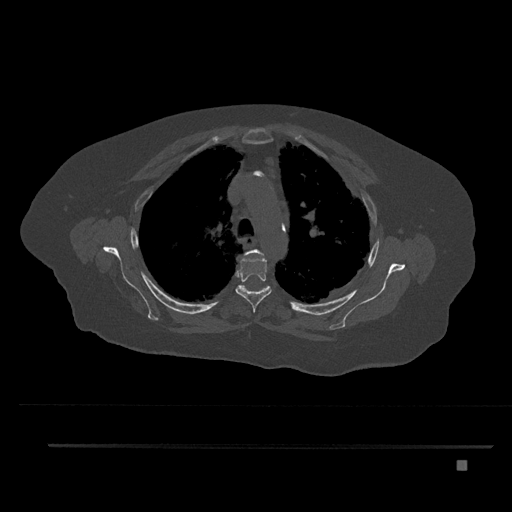
CT including the spine, one axial slice; slice 601 of 797 in the series (ordered by position); reconstruction kernel Br40s/3; bone window (W 1800 / L 400 HU); 0.5 mm slice thickness; 512 × 512 image matrix, field of view 437 × 437 mm. Female patient, age 76 years. Case-level facts recorded for this patient, not image findings: primary cancer: lung; vertebrae with lytic lesions (as recorded): T11, L3.
Outlined on this slice (semi-automatic segmentation, software-assisted and operator-edited):
- T3 vertebra: bounding box (x1, y1, x2, y2) in pixels: (243, 250, 264, 258)
- T4 vertebra: (235, 253, 272, 313)
- T5 vertebra: (238, 285, 267, 292)